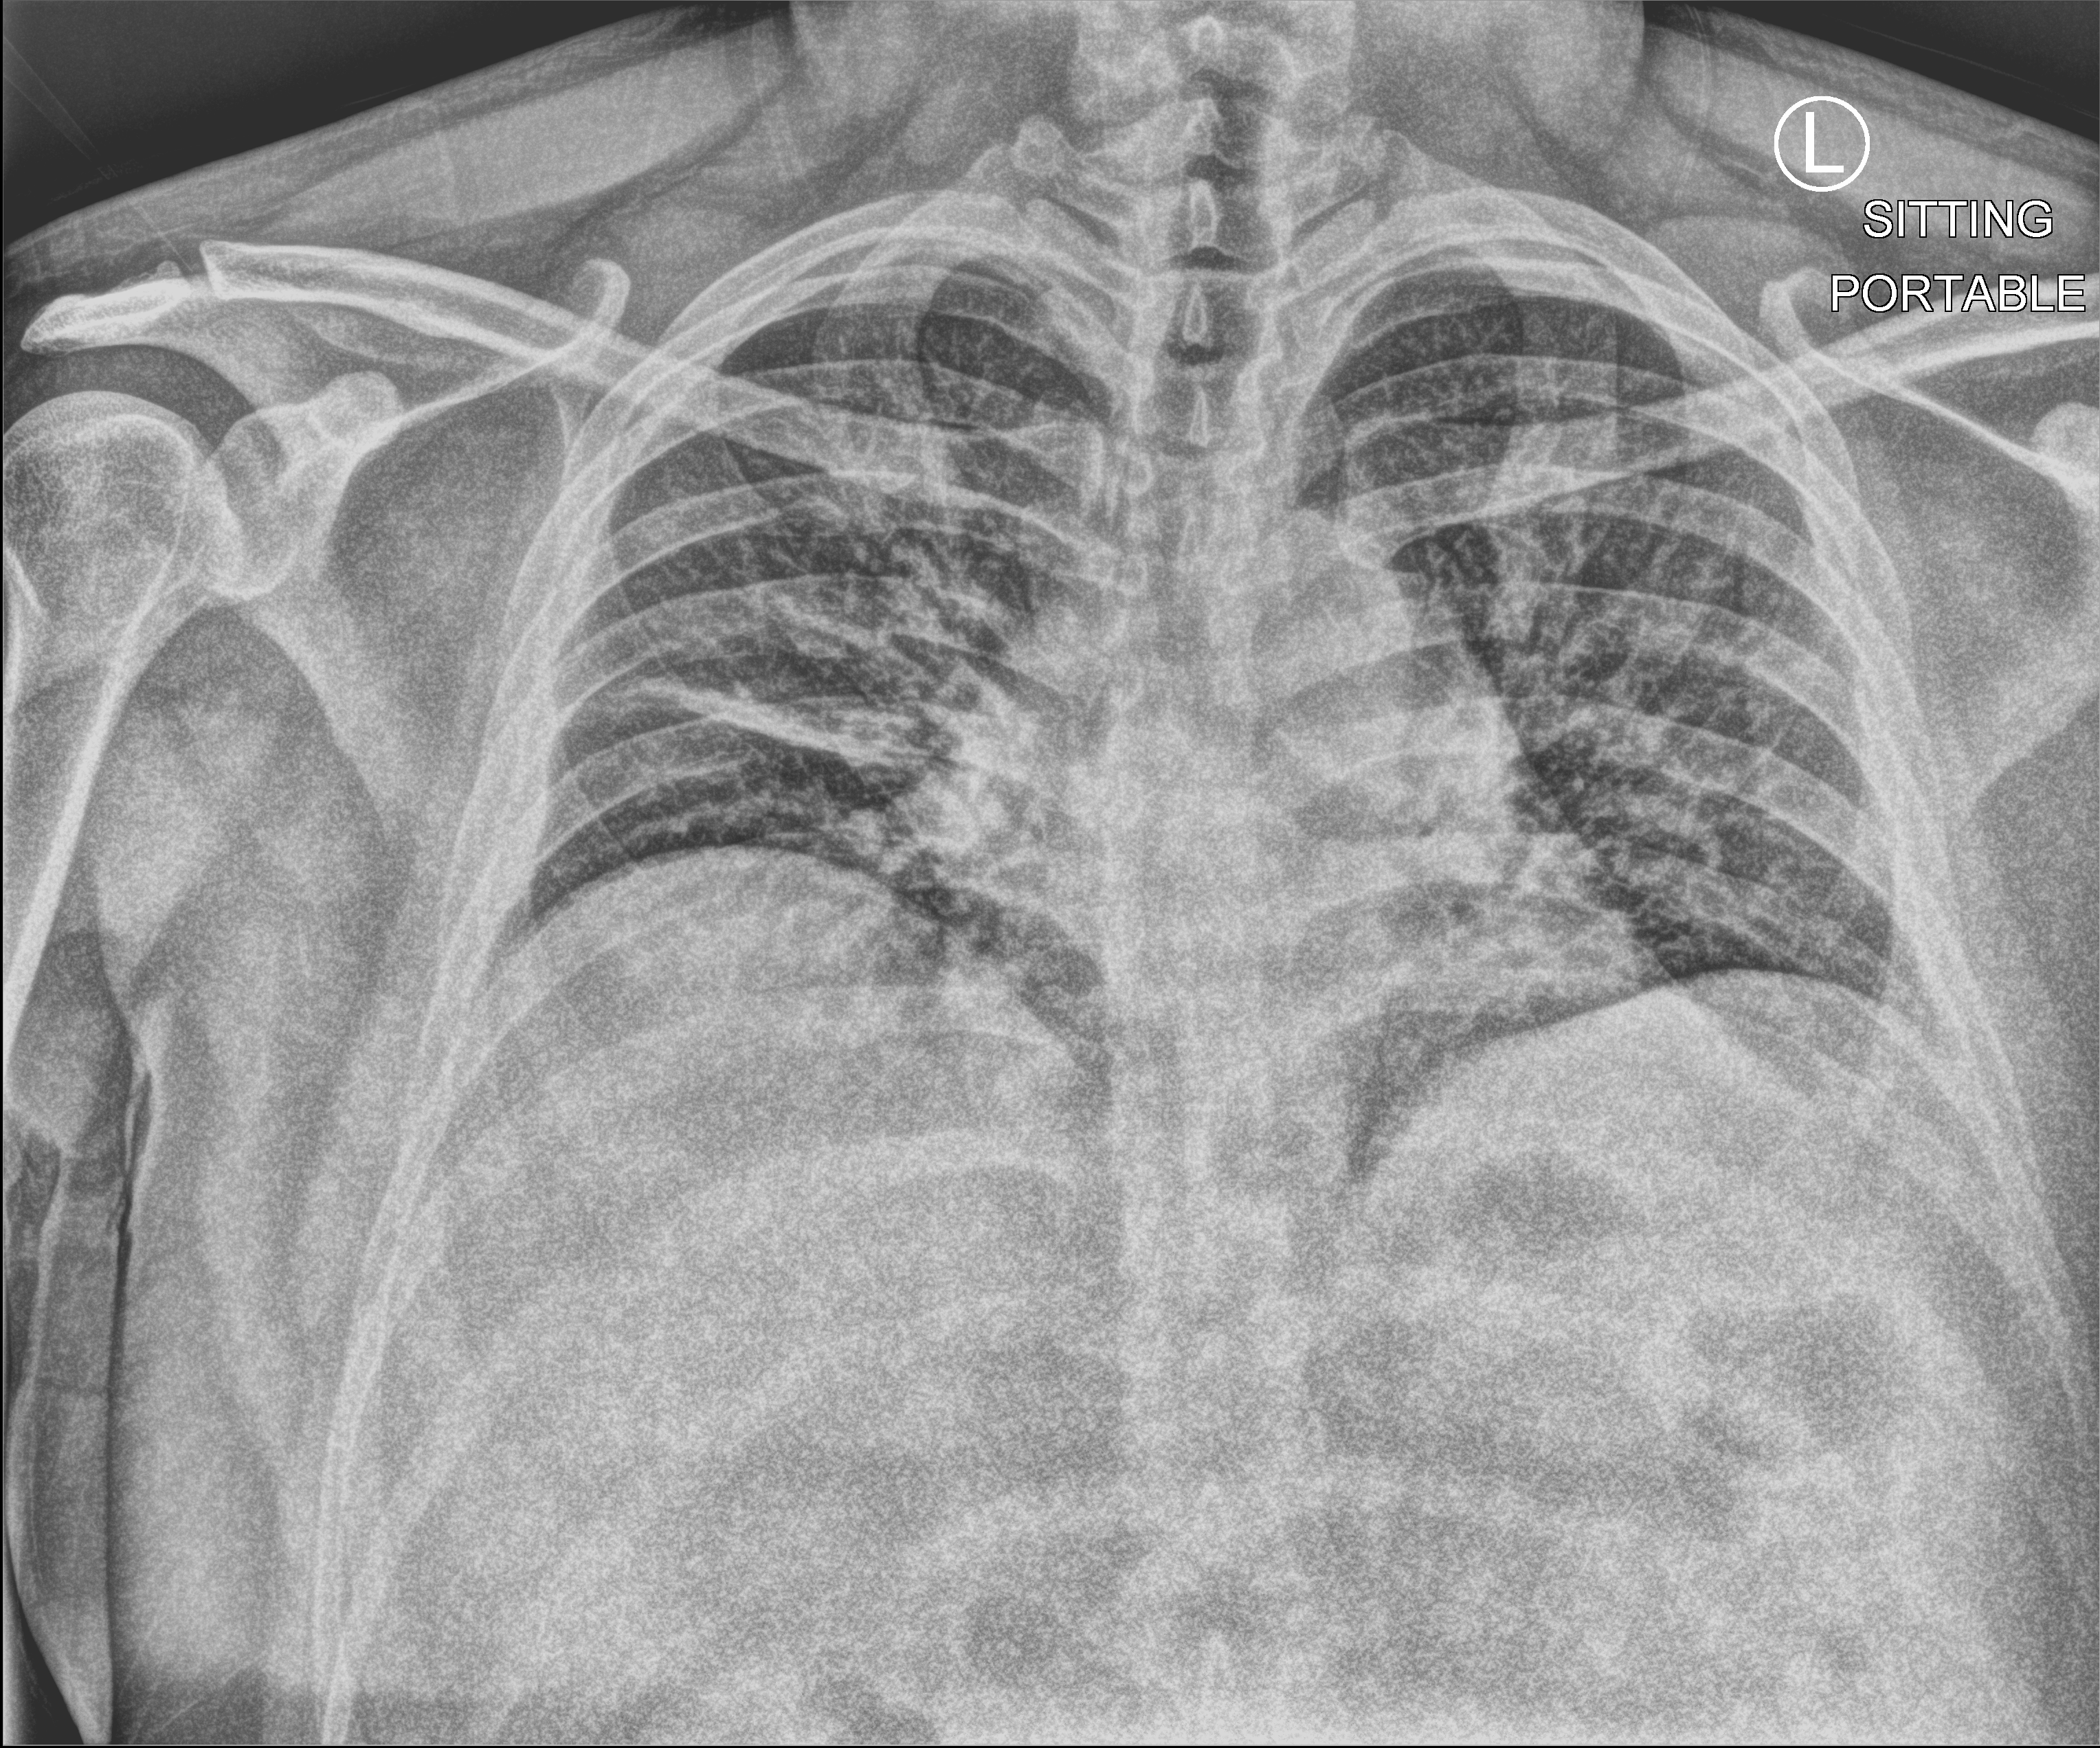
Bedside chest radiograph (computed radiography); anteroposterior (AP) projection. Patient hospitalised with COVID-19; male, aged 18–59 years.
Hospital-stay facts (about this admission, not read from this image; timing relative to this image not recorded):
- length of hospital stay: 1 day
- mechanically ventilated during this hospital stay: no